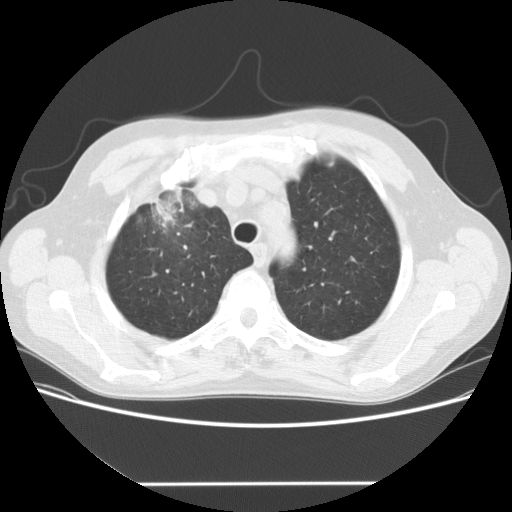
Low-dose screening chest CT, one axial slice. Position 125 of 153 along the scan axis. Reconstruction kernel STANDARD. 120 kVp. Lung window (W 1500 / L -600 HU). 2.5 mm slice thickness. 512 × 512 image matrix.
Structures marked on this image (manually delineated by an expert):
- lesion 1 (tumor, upper lobe of right lung): bounding box [x1, y1, x2, y2] px = [152, 194, 184, 230]